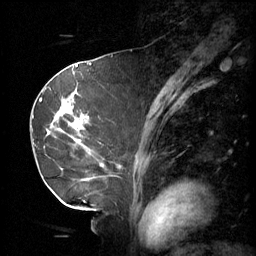
Breast MRI (dynamic contrast-enhanced), one sagittal slice; position 28 of 60 along the scan axis; 3 images stored at this slice position (order not interpretable as contrast timing); 1.5 T; TE 4.2 ms, TR 11 ms; 256 × 256 image matrix, field of view 220 × 220 mm. Patient: female, 69 years.
Structures marked on this image (semi-automatically segmented with operator editing):
- analysis volume of interest (the breast-tissue region the enhancement analysis was run in; not a lesion): box from (x=36, y=88) to (x=116, y=189) px
- tumour enhancement mask (voxels above the 70 % enhancement threshold inside the analysis volume of interest): (x=40, y=98)–(x=104, y=167)